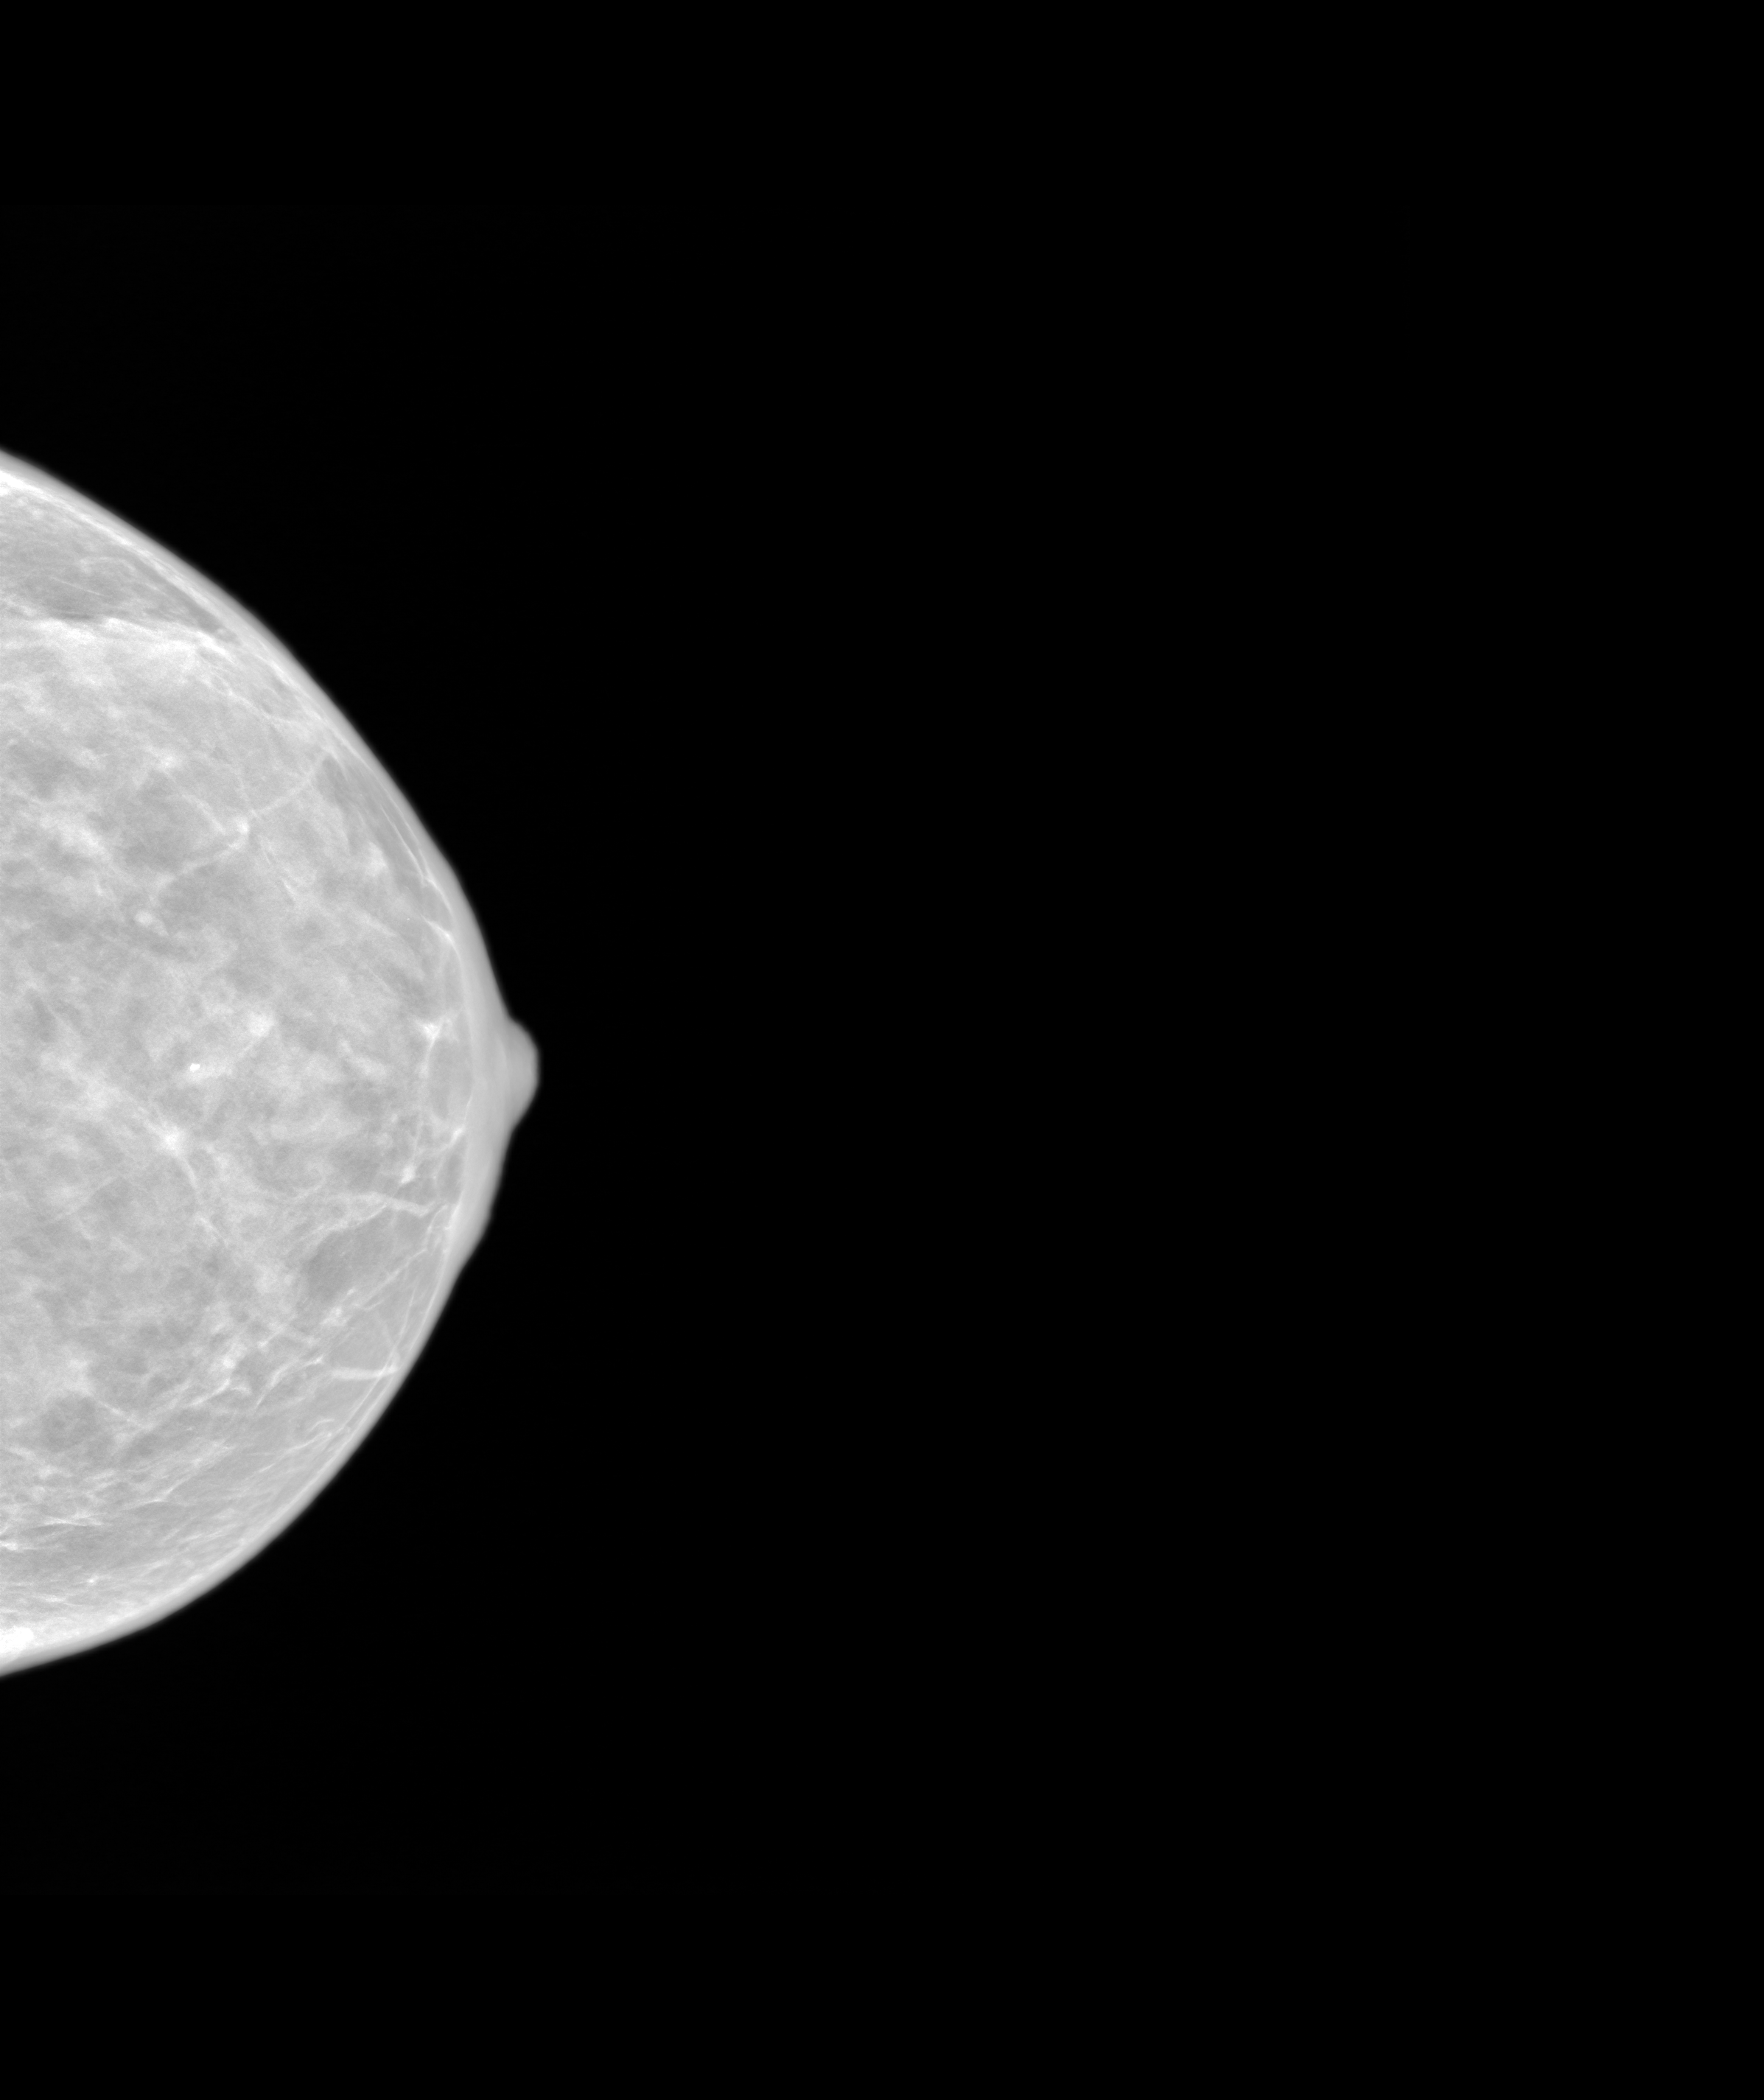
Screening examination. Female patient, age 43 years.
Image type: synthesized 2-D view from tomosynthesis. Breast: left. Projection: cranio-caudal projection.